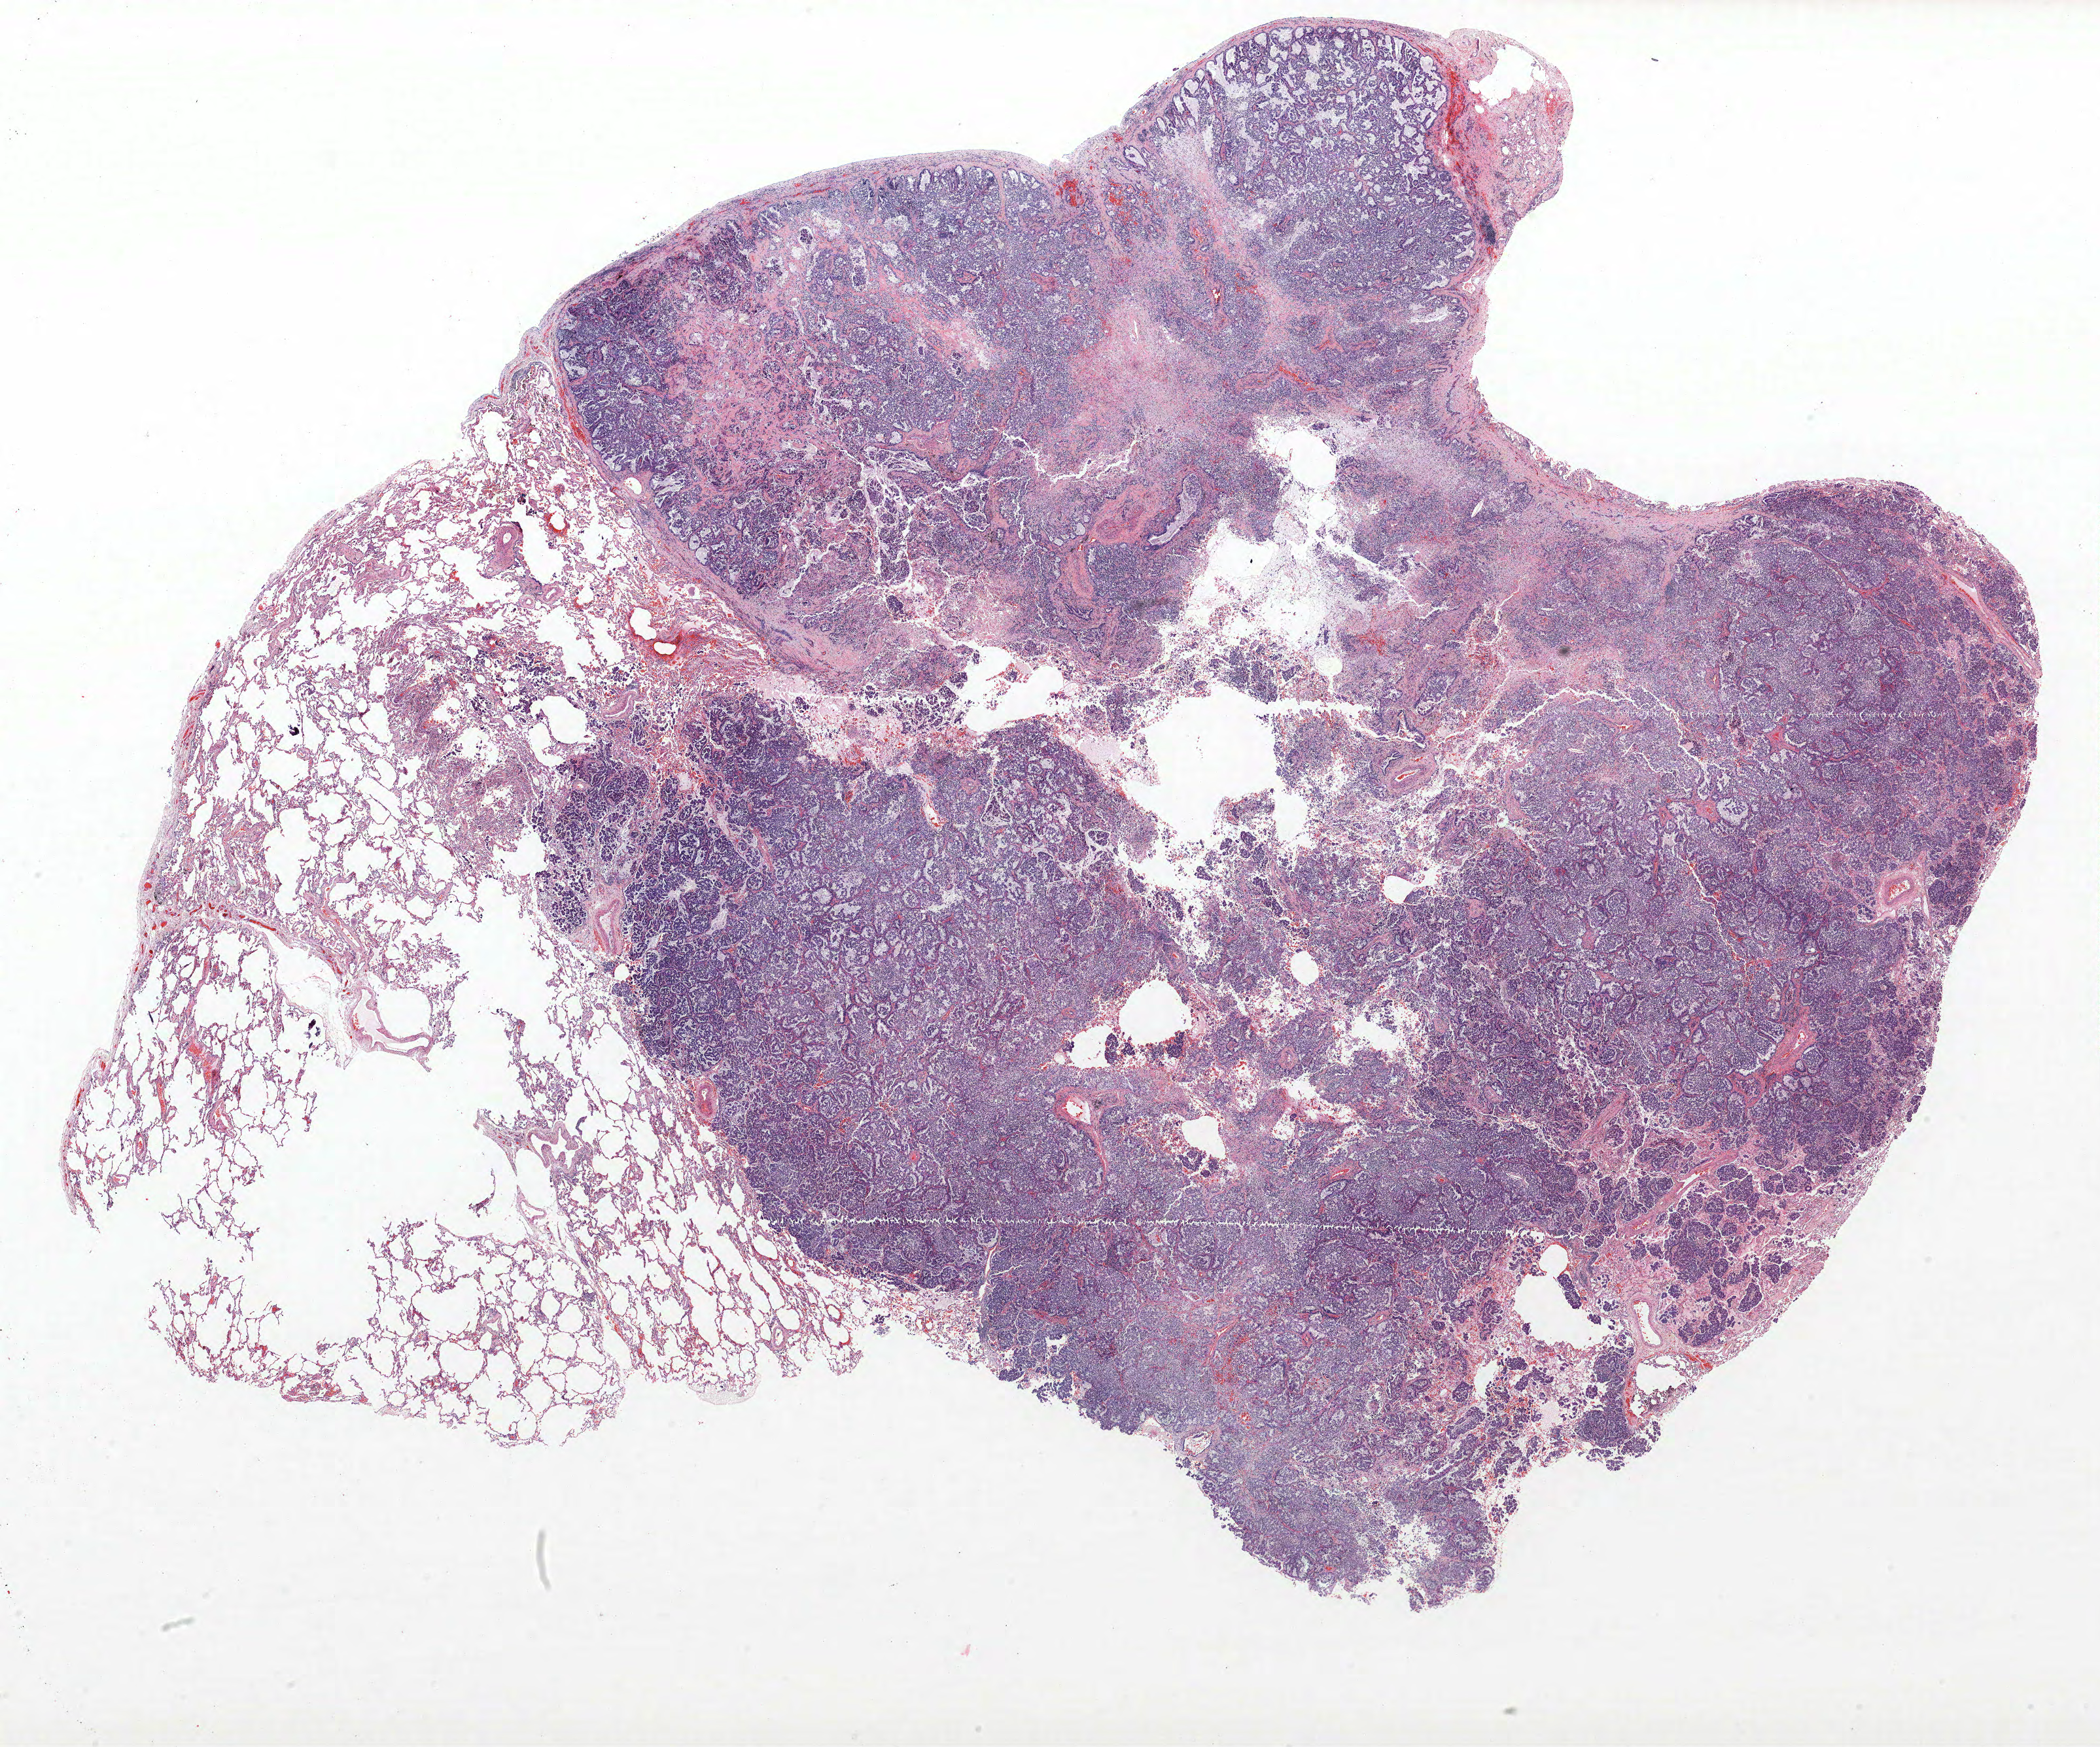
Whole-slide histology image, H&E — a low-resolution overview of the entire scanned area, about 25.7 x 21.4 mm, FFPE section, lung. Male patient, aged 74 at enrolment. Grade: well differentiated (G1).
Stage (AJCC 6th edition): IA. Tumour size (pathology): 20 mm. Participant's lung-cancer diagnosis: Papillary adenocarcinoma, NOS (ICD-O-3 8260/3). Primary tumour location (clinical record): right middle lobe.